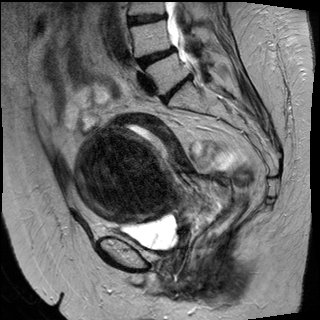
Pelvic MRI for cervical cancer, one sagittal slice. Position 24 of 50 along the scan axis. T2-weighted. 1.5 T. TE 89 ms, TR 4880 ms. 320 × 320 image matrix. Female patient, age 50 years.
Outlined on this slice (outlined manually by an expert reader):
- uterus and cervix: bounding box [x1, y1, x2, y2] px = [72, 113, 231, 236]